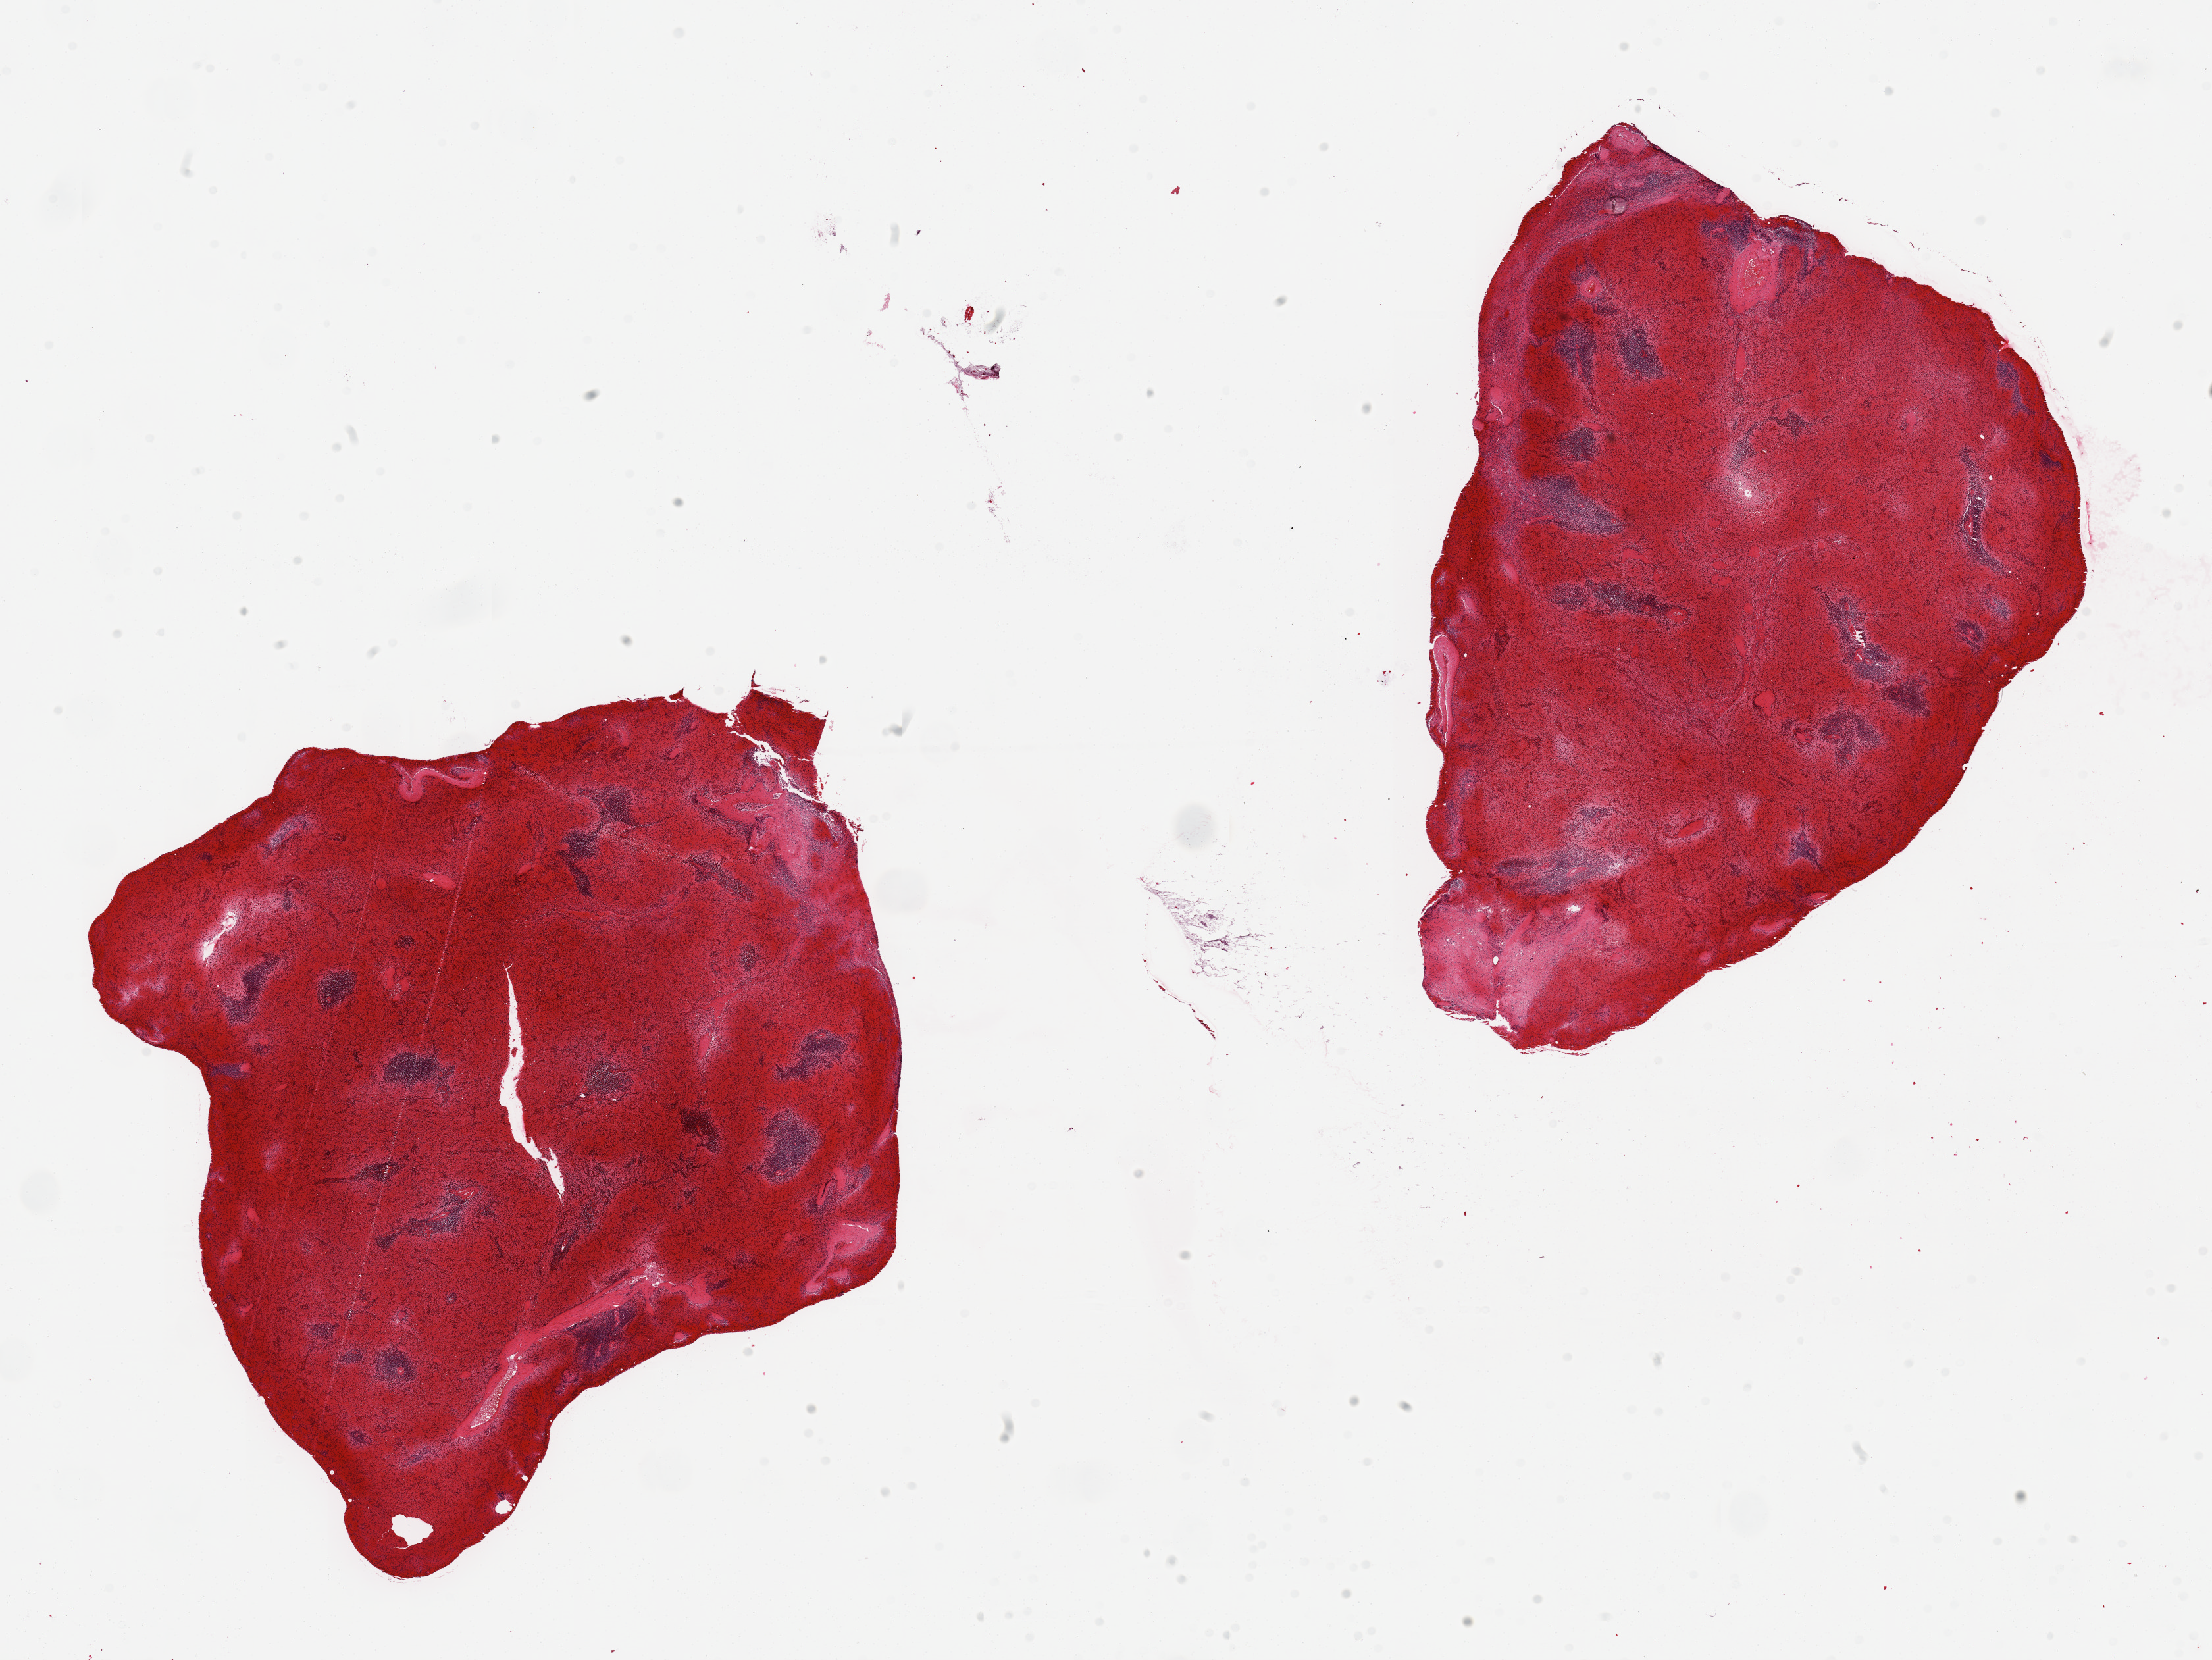
Hematoxylin and eosin (H&E) whole-slide image, shown as a low-resolution overview of the whole scanned area (about 26.6 x 19.9 mm, slide scanned at 20x). PAXgene-fixed paraffin-embedded (PFPE) section. Sampled site (target tissue): spleen. Tissue donor sample.
- pathologist's review note for this sample: 2 pieces, congested, autolyzed